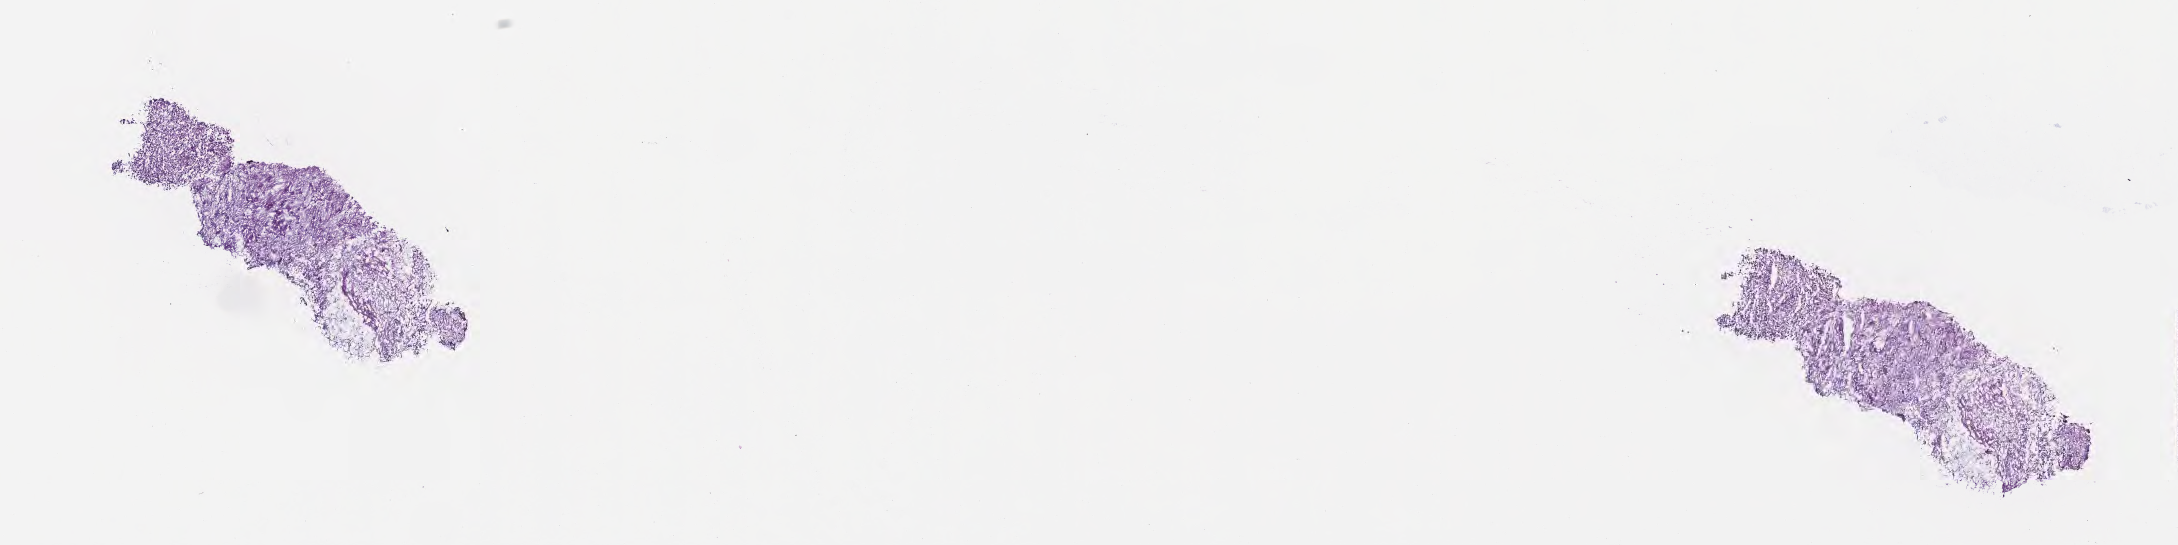
Hematoxylin and eosin (H&E) whole-slide image, whole scanned area (about 17.6 x 4.4 mm) shown as a low-resolution overview, frozen section (tissue freezing medium), recurrent tumor, site: brain. Female patient; age at initial diagnosis 63 years. Composition of this section per pathologist review: tumor cells 49%, tumor nuclei 82%.
Patient diagnosis: Glioblastoma, NOS.